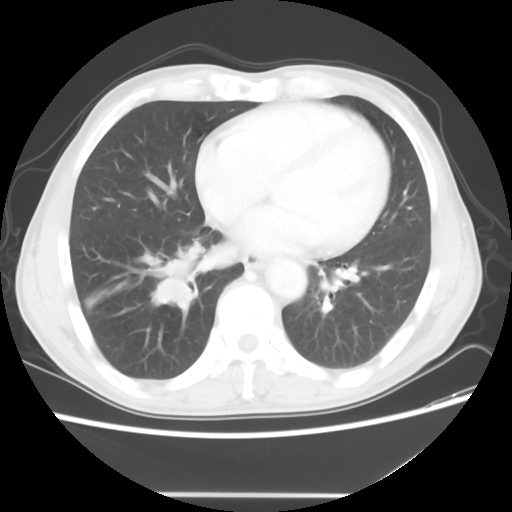
Chest CT, one axial slice. Slice 21 of 56 in the series (ordered by position). Reconstruction kernel STANDARD. 120 kVp. Lung window (W 1500 / L -600 HU). 5 mm slice thickness. 512 × 512 image matrix, field of view 344 × 344 mm. Patient: male, 65 years. Case-level facts recorded for this patient, not image findings: clinical TNM (as recorded): T1c N3 M0; histopathological grade: G3.
Annotated regions visible in this slice (bounding box drawn by a radiologist):
- lung tumour (recorded histology: small cell carcinoma): bounding box [x1, y1, x2, y2] px = [144, 235, 214, 319]